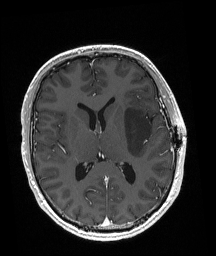
Brain MRI from a brain-tumour surgery series, one axial slice; T1-weighted post-contrast; 216 × 256 image matrix. Case-level facts recorded for this patient, not image findings: histopathology: Astrocytoma; WHO grade: 3; IDH mutation: yes; tumour location: Left Posterior Frontal.
Outlined on this slice (outlined manually by an expert reader):
- tumour: bounding box (x1, y1, x2, y2) in pixels: (124, 109, 152, 157)